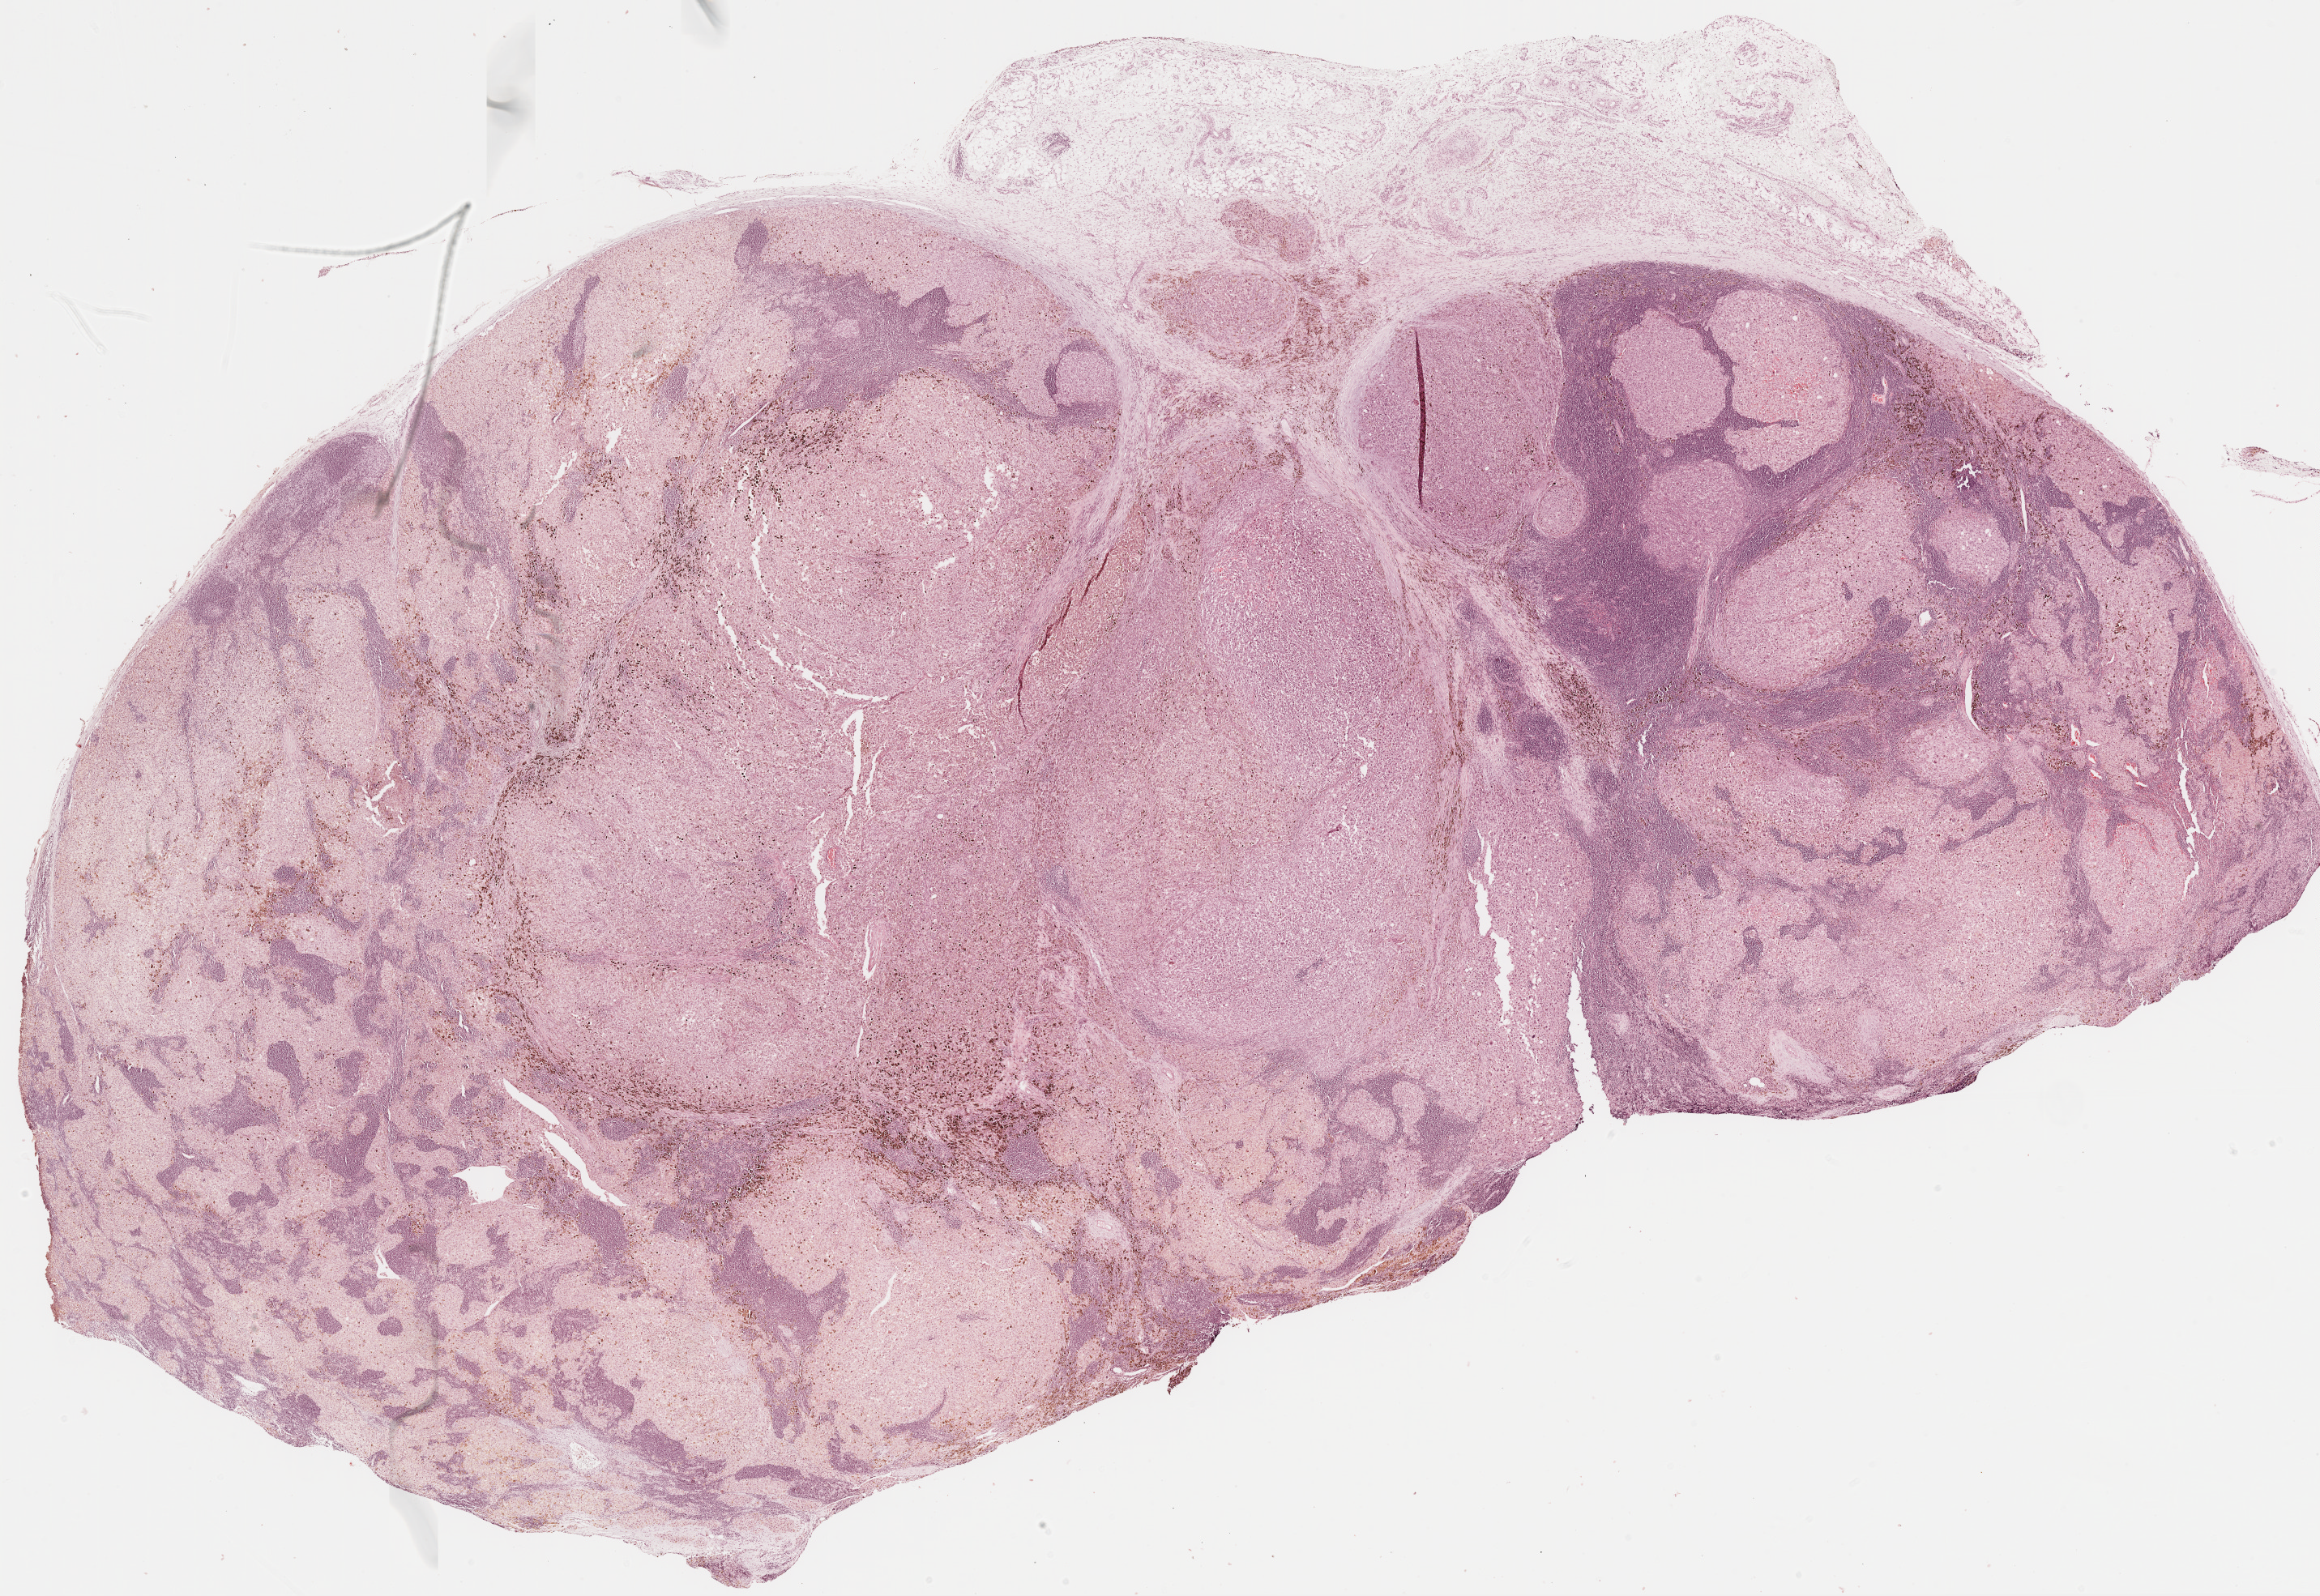
Whole-slide histology image, H&E-stained — whole scanned area (about 23.1 x 15.9 mm, from a 20x scan) shown as a low-resolution overview; formalin-fixed paraffin-embedded (FFPE) diagnostic section; metastatic tumour sample. Patient sex: male.
This section: metastatic tumour tissue. Patient diagnosis: Malignant melanoma, NOS.